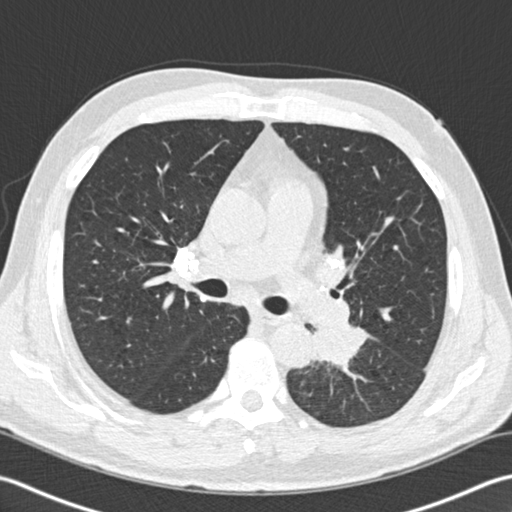
Low-dose screening chest CT, one axial slice. Position 105 of 170 along the scan axis. 120 kVp. Lung window (W 1500 / L -600 HU). 2 mm slice thickness. 512 × 512 image matrix, field of view 350 × 350 mm.
Outlined on this slice (expert manual segmentation):
- lesion 1 (tumor, lower lobe of left lung): box from (x=315, y=319) to (x=368, y=368) px